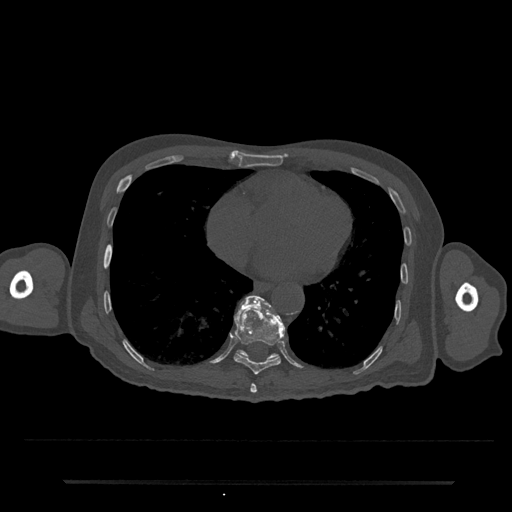
CT including the spine, one axial slice; reconstruction kernel Br40s/3; 120 kVp; bone window (W 1800 / L 400 HU); 512 × 512 image matrix. Patient: male, 74 years. Case-level facts recorded for this patient, not image findings: primary cancer: prostate.
Annotated regions visible in this slice (semi-automatically segmented with operator editing):
- T10 vertebra: bounding box <237,295,278,360> (left, top, right, bottom; pixels)
- T8 vertebra: <250,383,257,394>
- T9 vertebra: <234,296,285,375>